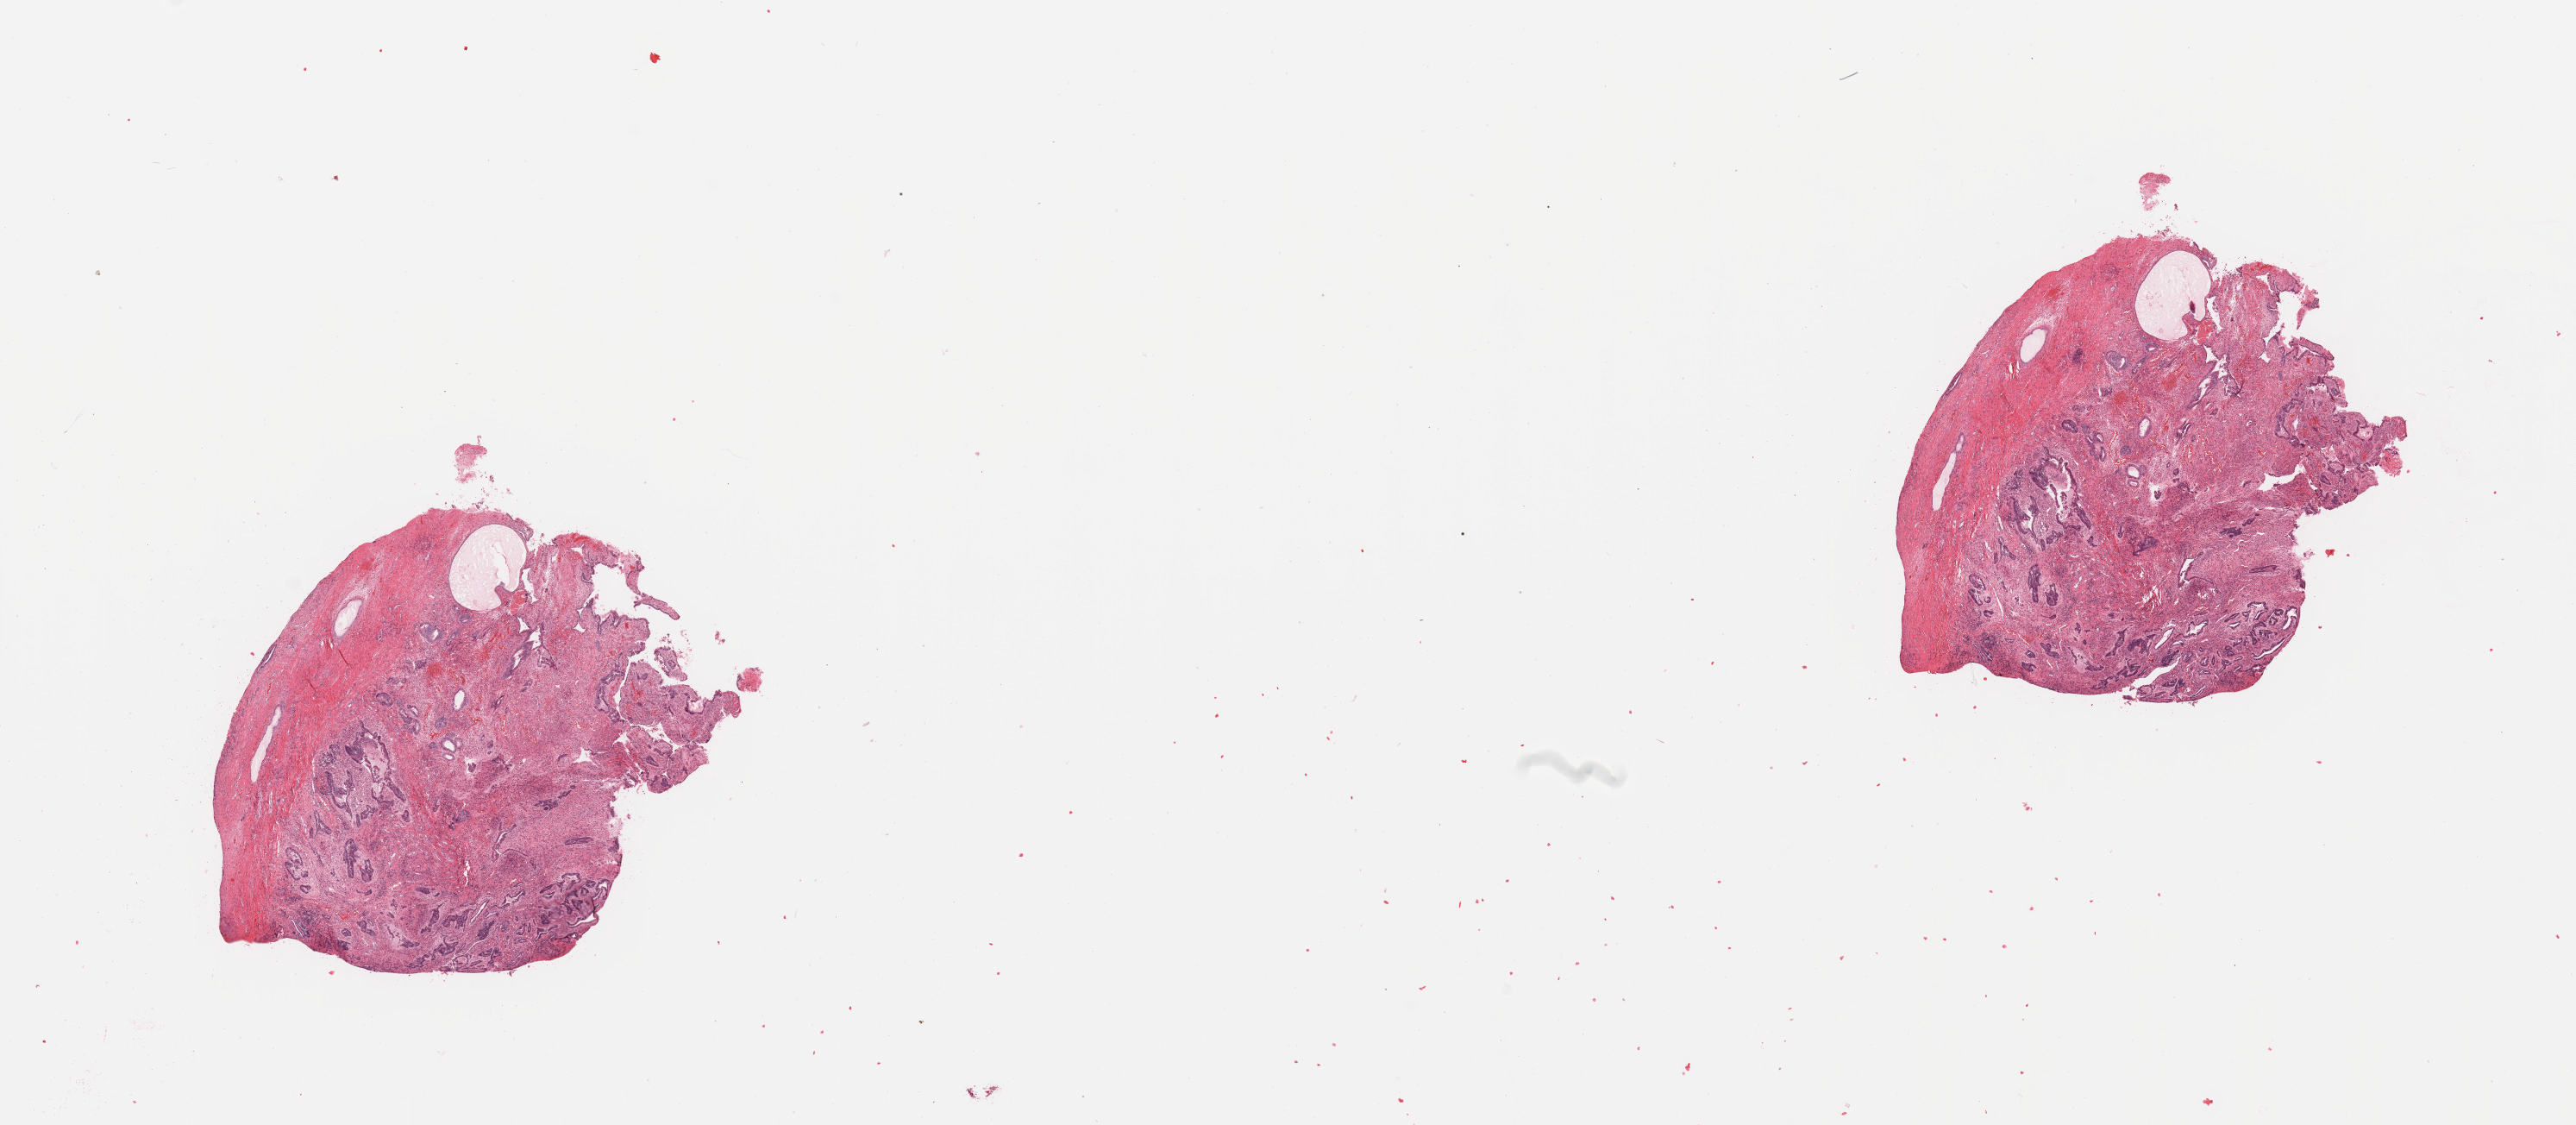
Whole-slide histology image, H&E — low-resolution overview of the scanned area, about 23.6 x 10.3 mm (from a 20x scan). Tumour tissue sample, uterus. Patient: female, age 56 years. Histologic grade: G1 (well differentiated).
Diagnosis: Endometrioid adenocarcinoma, NOS. Primary tumour site (as recorded): anterior endometrium. AJCC pathologic stage: I.